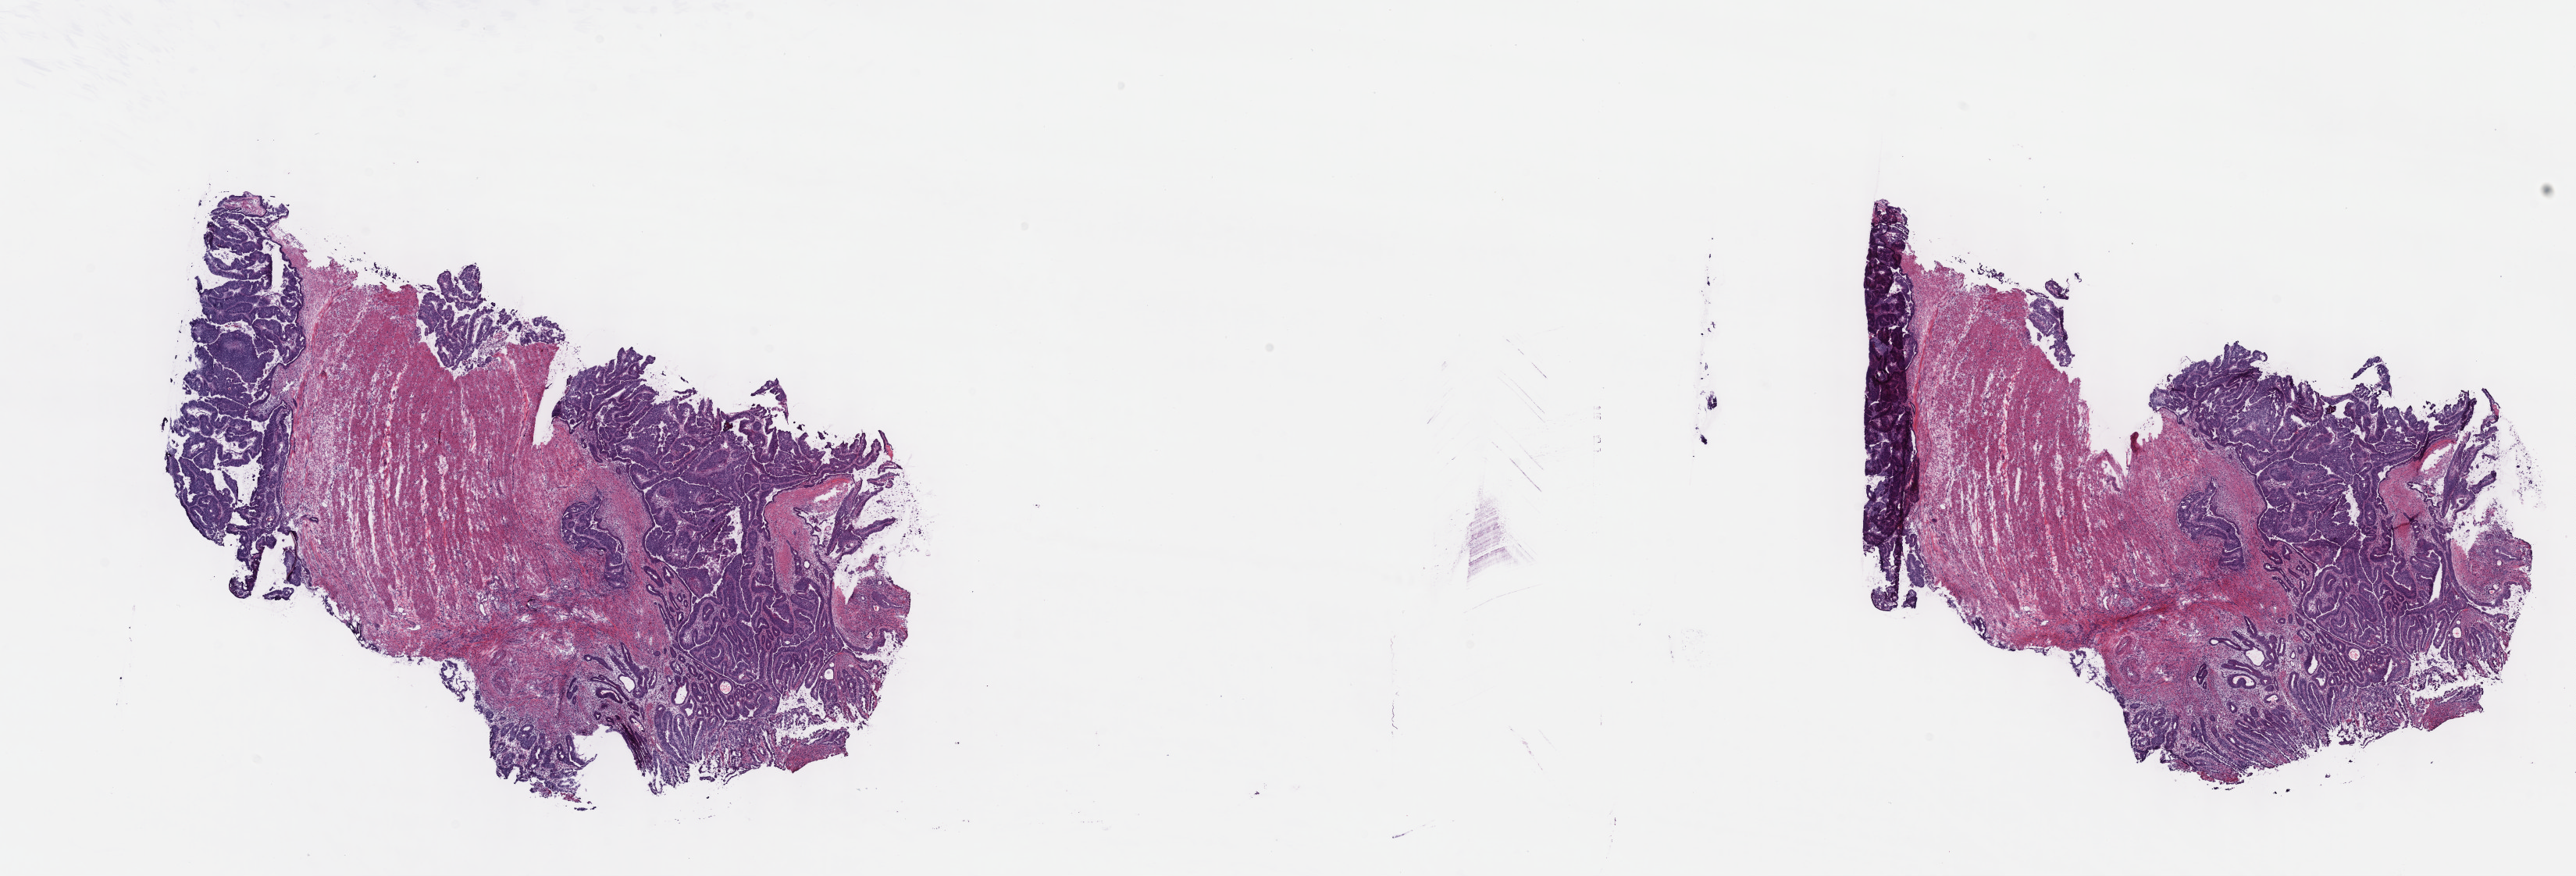
Hematoxylin and eosin (H&E) stained whole-slide image, low-resolution overview of the scanned area, about 26.7 x 9.1 mm; frozen section from the top of the tissue portion; primary tumour sample from the colon. Female, age 53 years at initial diagnosis. Pathologist review of this section (percent, as recorded): tumour cells 26%, tumour nuclei 80%, normal cells 0%, stromal cells 70%, necrosis 4%. Inflammatory infiltration, as recorded: lymphocyte infiltration 6%, monocyte infiltration 2%, neutrophil infiltration 2%.
AJCC pathologic stage: IIA (7th edition). Pathologic diagnosis: Adenocarcinoma, NOS (sigmoid colon). Lymph nodes positive (case pathology): 0 of 18 examined.